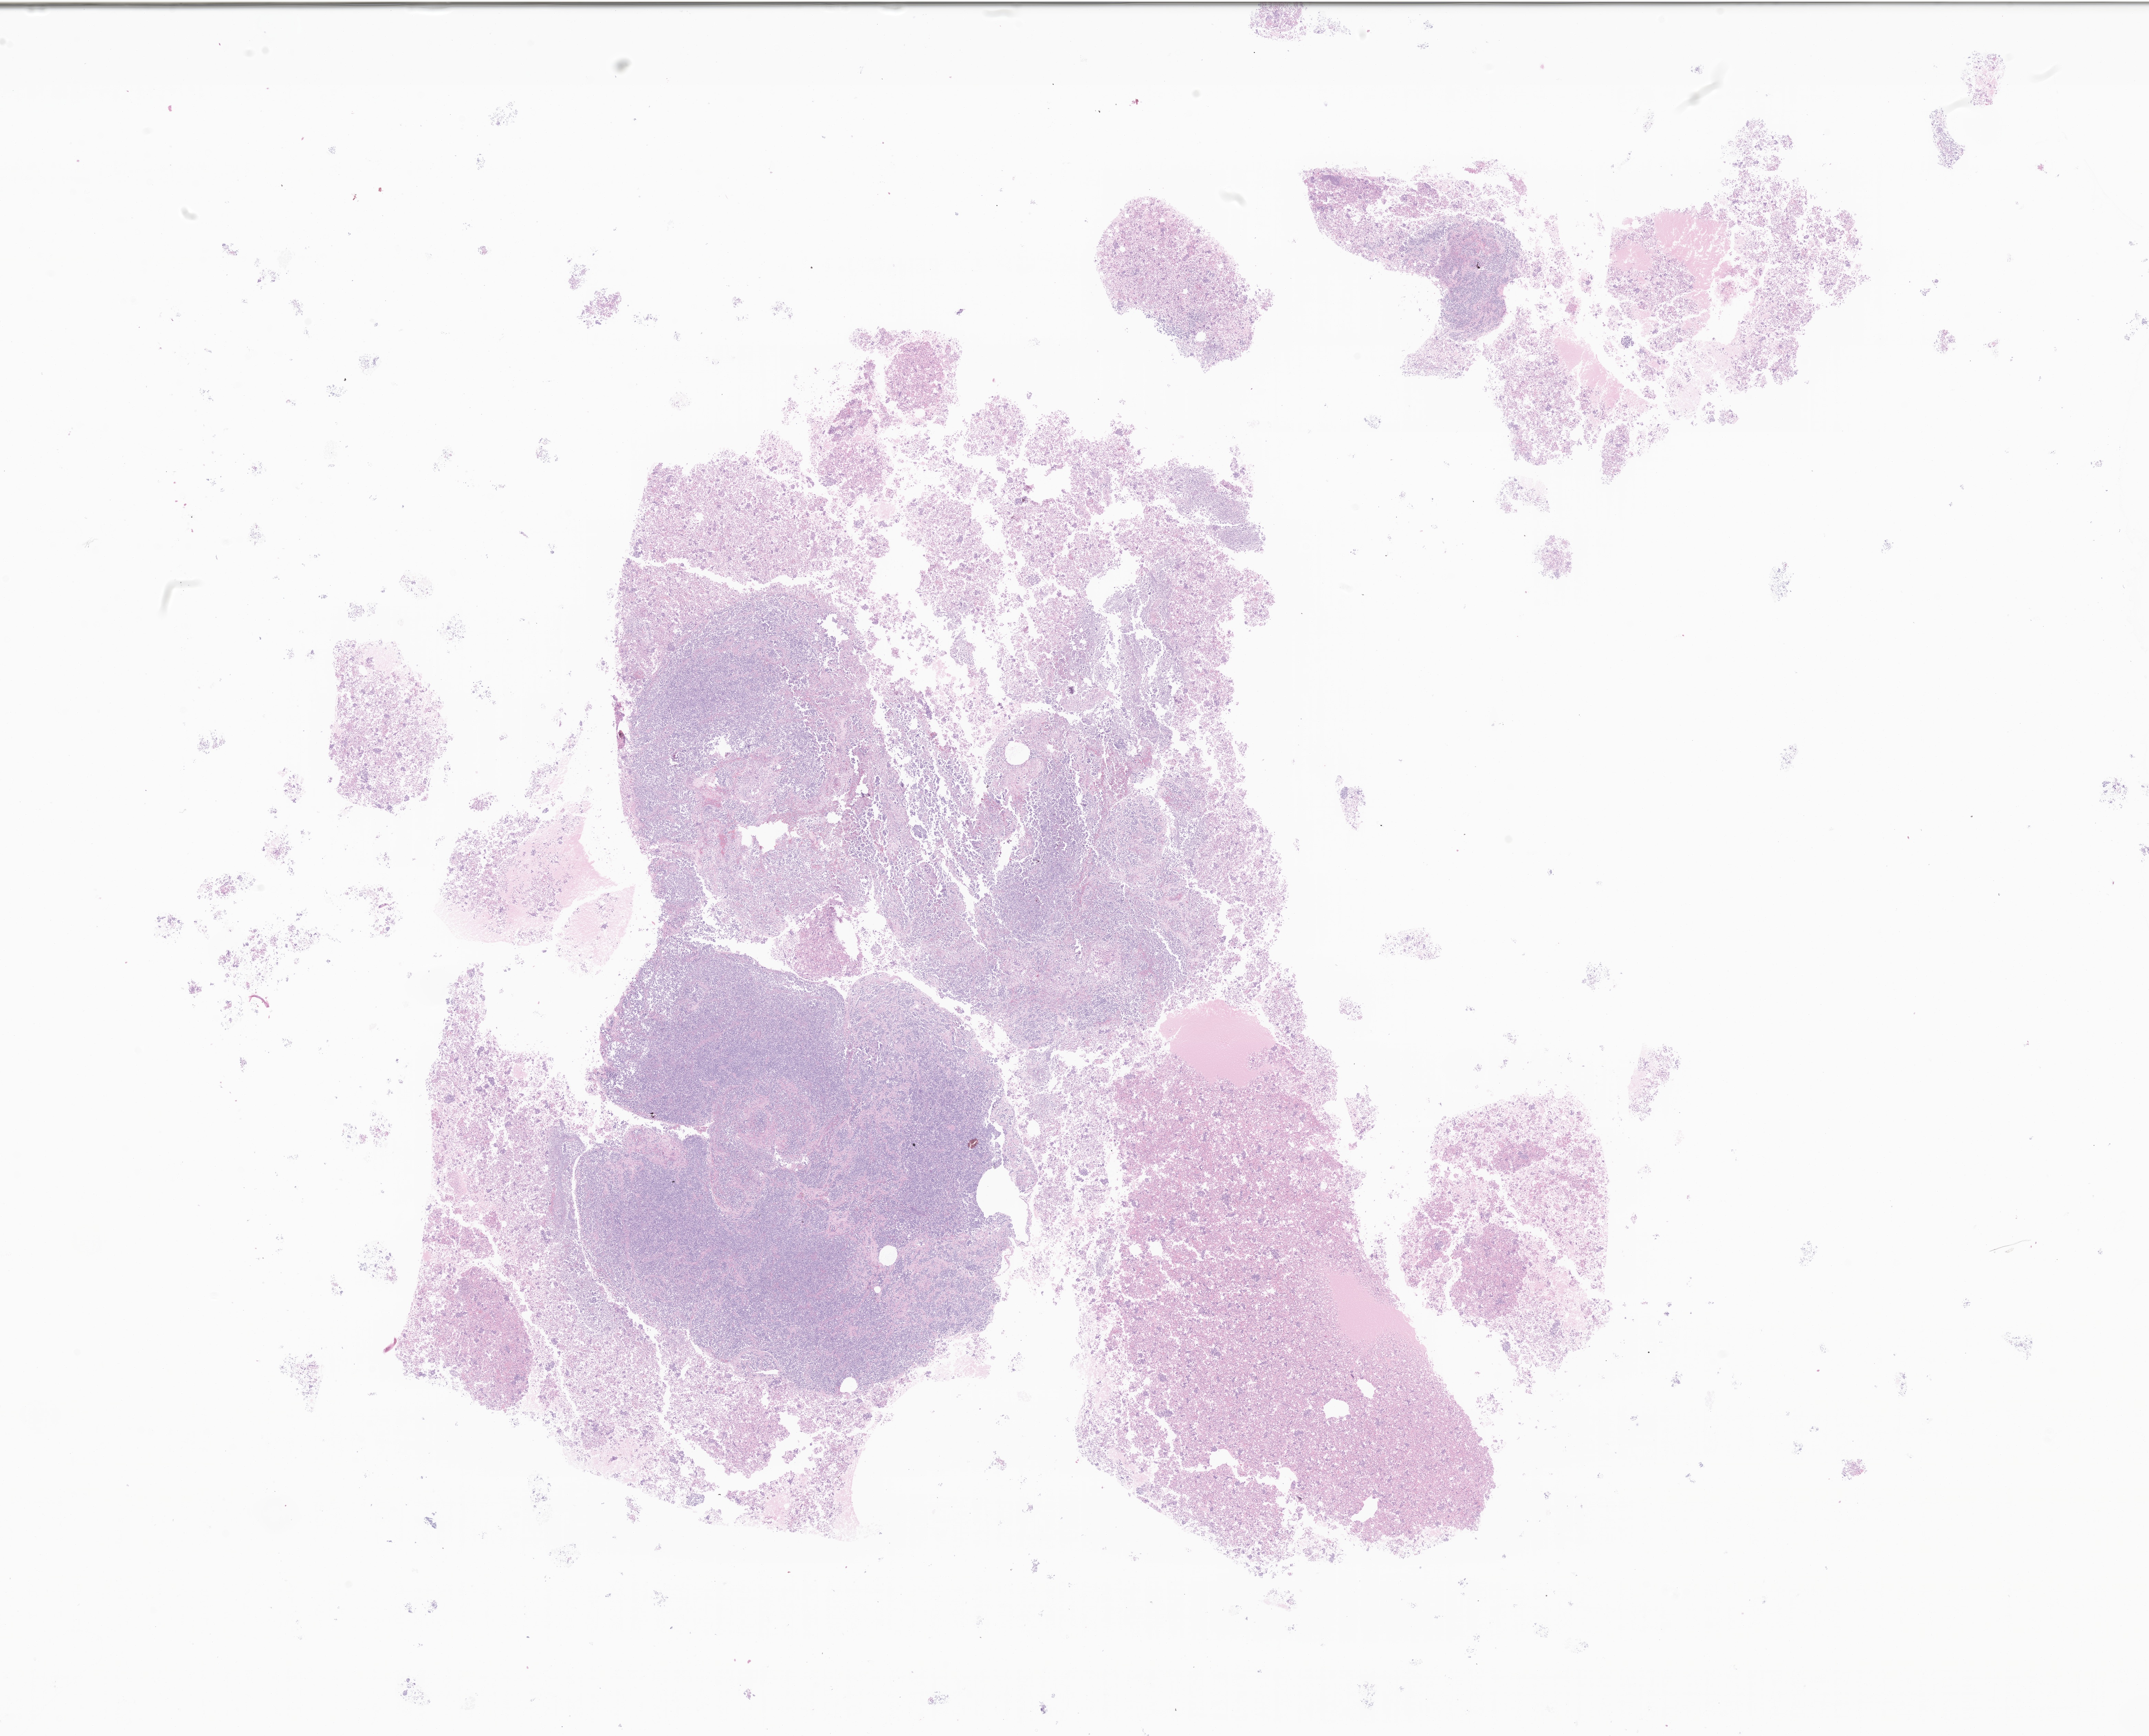
Whole-slide image, H&E stain of tumor tissue from the pleura — a low-resolution overview of the entire scanned area, about 26.4 x 21.3 mm; formalin-fixed paraffin-embedded section. Patient female; age 104 months (8 years 8 months).
Diagnosis (ICD-O-3 morphology term): Sarcoma, NOS.